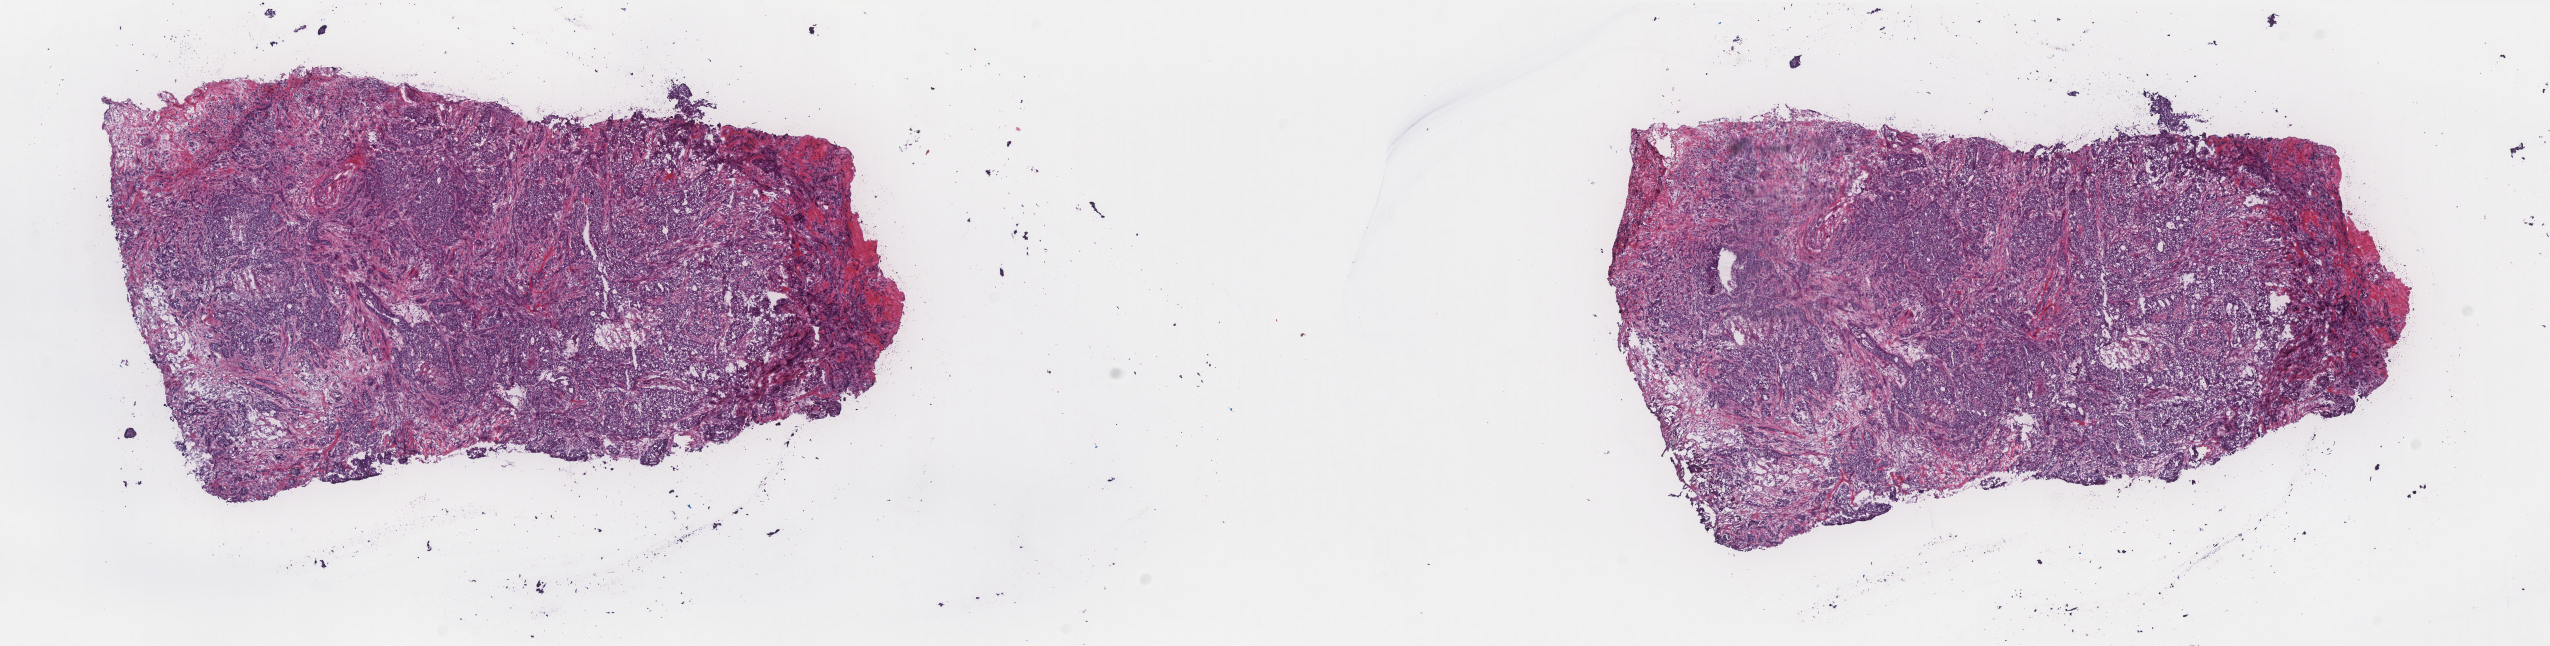
H&E whole-slide image — shown as a low-resolution overview of the whole scanned area (about 20.4 x 5.2 mm), frozen section from the top of the tissue portion, primary tumour sample from the breast. Patient sex: female. Composition of this section per pathologist review: tumour cells 85%, tumour nuclei 85%, normal cells 0%, stromal cells 15%, necrosis 0%. Infiltration values recorded for this section: lymphocyte infiltration 3%, monocyte infiltration 1%, neutrophil infiltration 1%.
Laterality: left. AJCC pathologic stage: IIA (7th edition). Lymph nodes positive (case pathology): 0 of 13 examined. Pathologic diagnosis: Infiltrating duct carcinoma, NOS.